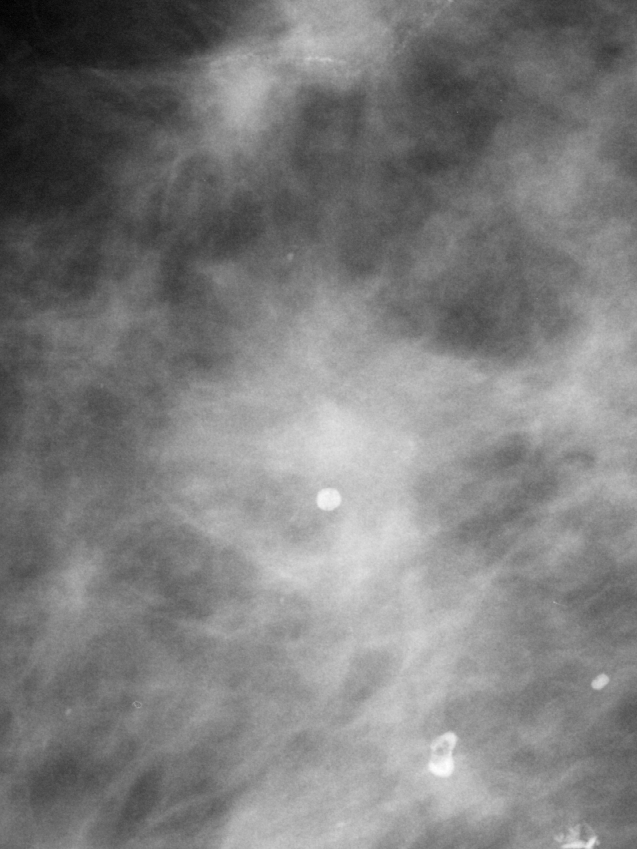
Crop from a digitized film mammogram around one marked abnormality; right breast; MLO view; BI-RADS breast density category 2 (scale 1–4).
Finding: mass, shape asymmetric breast tissue, margins ill defined; BI-RADS assessment category 5; pathology result (as recorded, not read from the image): malignant.